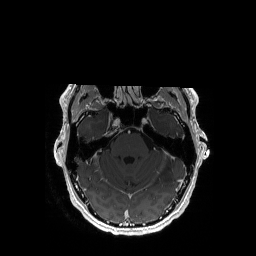
Brain MRI from a brain-tumour surgery series, one axial slice. Position 123 of 192 along the scan axis. T1-weighted post-contrast. 1 mm slice thickness. 256 × 256 image matrix, field of view 256 × 256 mm. Case-level facts recorded for this patient, not image findings: histopathology: Astrocytoma; WHO grade: 3; IDH mutation: yes.
Structures marked on this image (expert manual segmentation):
- tumour: bounding box (x1, y1, x2, y2) in pixels: (155, 124, 176, 181)